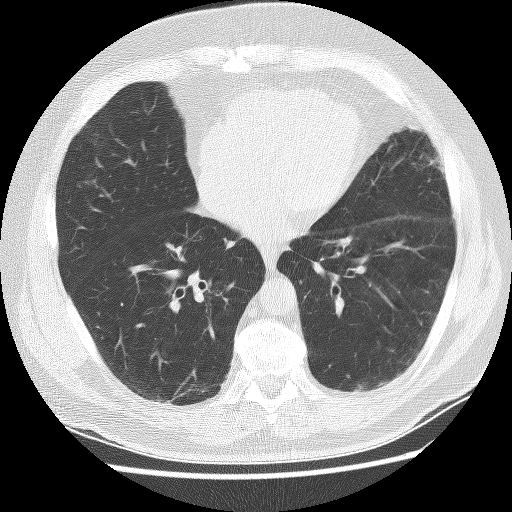
Axial slice from a low-dose chest CT screening exam; baseline screening round; lung window (W 1500 / L -600 HU); 2.5 mm slice thickness. Male participant, aged 65 years at enrolment. Former smoker at enrolment.
Expert-annotated lung lesion, bounding box <350,369,391,405> (left, top, right, bottom; pixels). No non-calcified nodule or mass ≥4 mm was recorded by the screening reader at this exam.